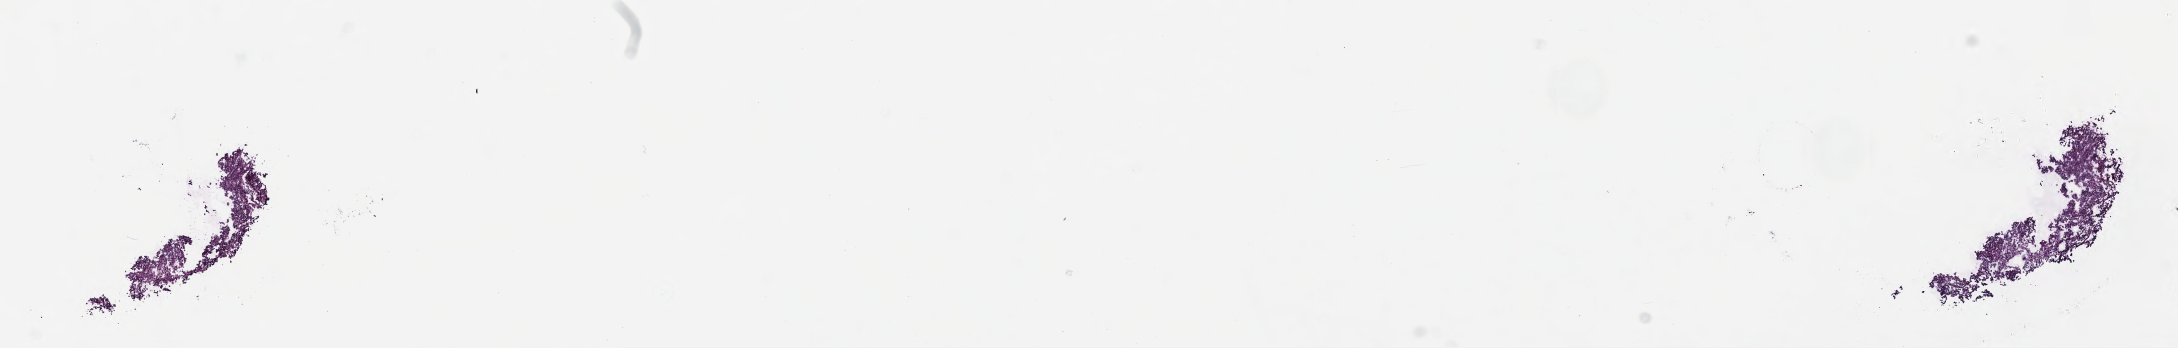
H&E whole-slide image — low-resolution overview of the scanned area, about 17.6 x 2.8 mm. Cryosection. Specimen: primary tumor. Site: kidney. Female patient; age at initial diagnosis 7 years. Slide review estimates, as recorded: tumor cells 95%, tumor nuclei 95%, stromal cells 5%, necrosis 0%, normal cells 0%. Inflammatory infiltration, as recorded: lymphocyte infiltration 0%, monocyte infiltration 0%, neutrophil infiltration 0%.
Histologic diagnosis: Nephroblastoma, NOS.